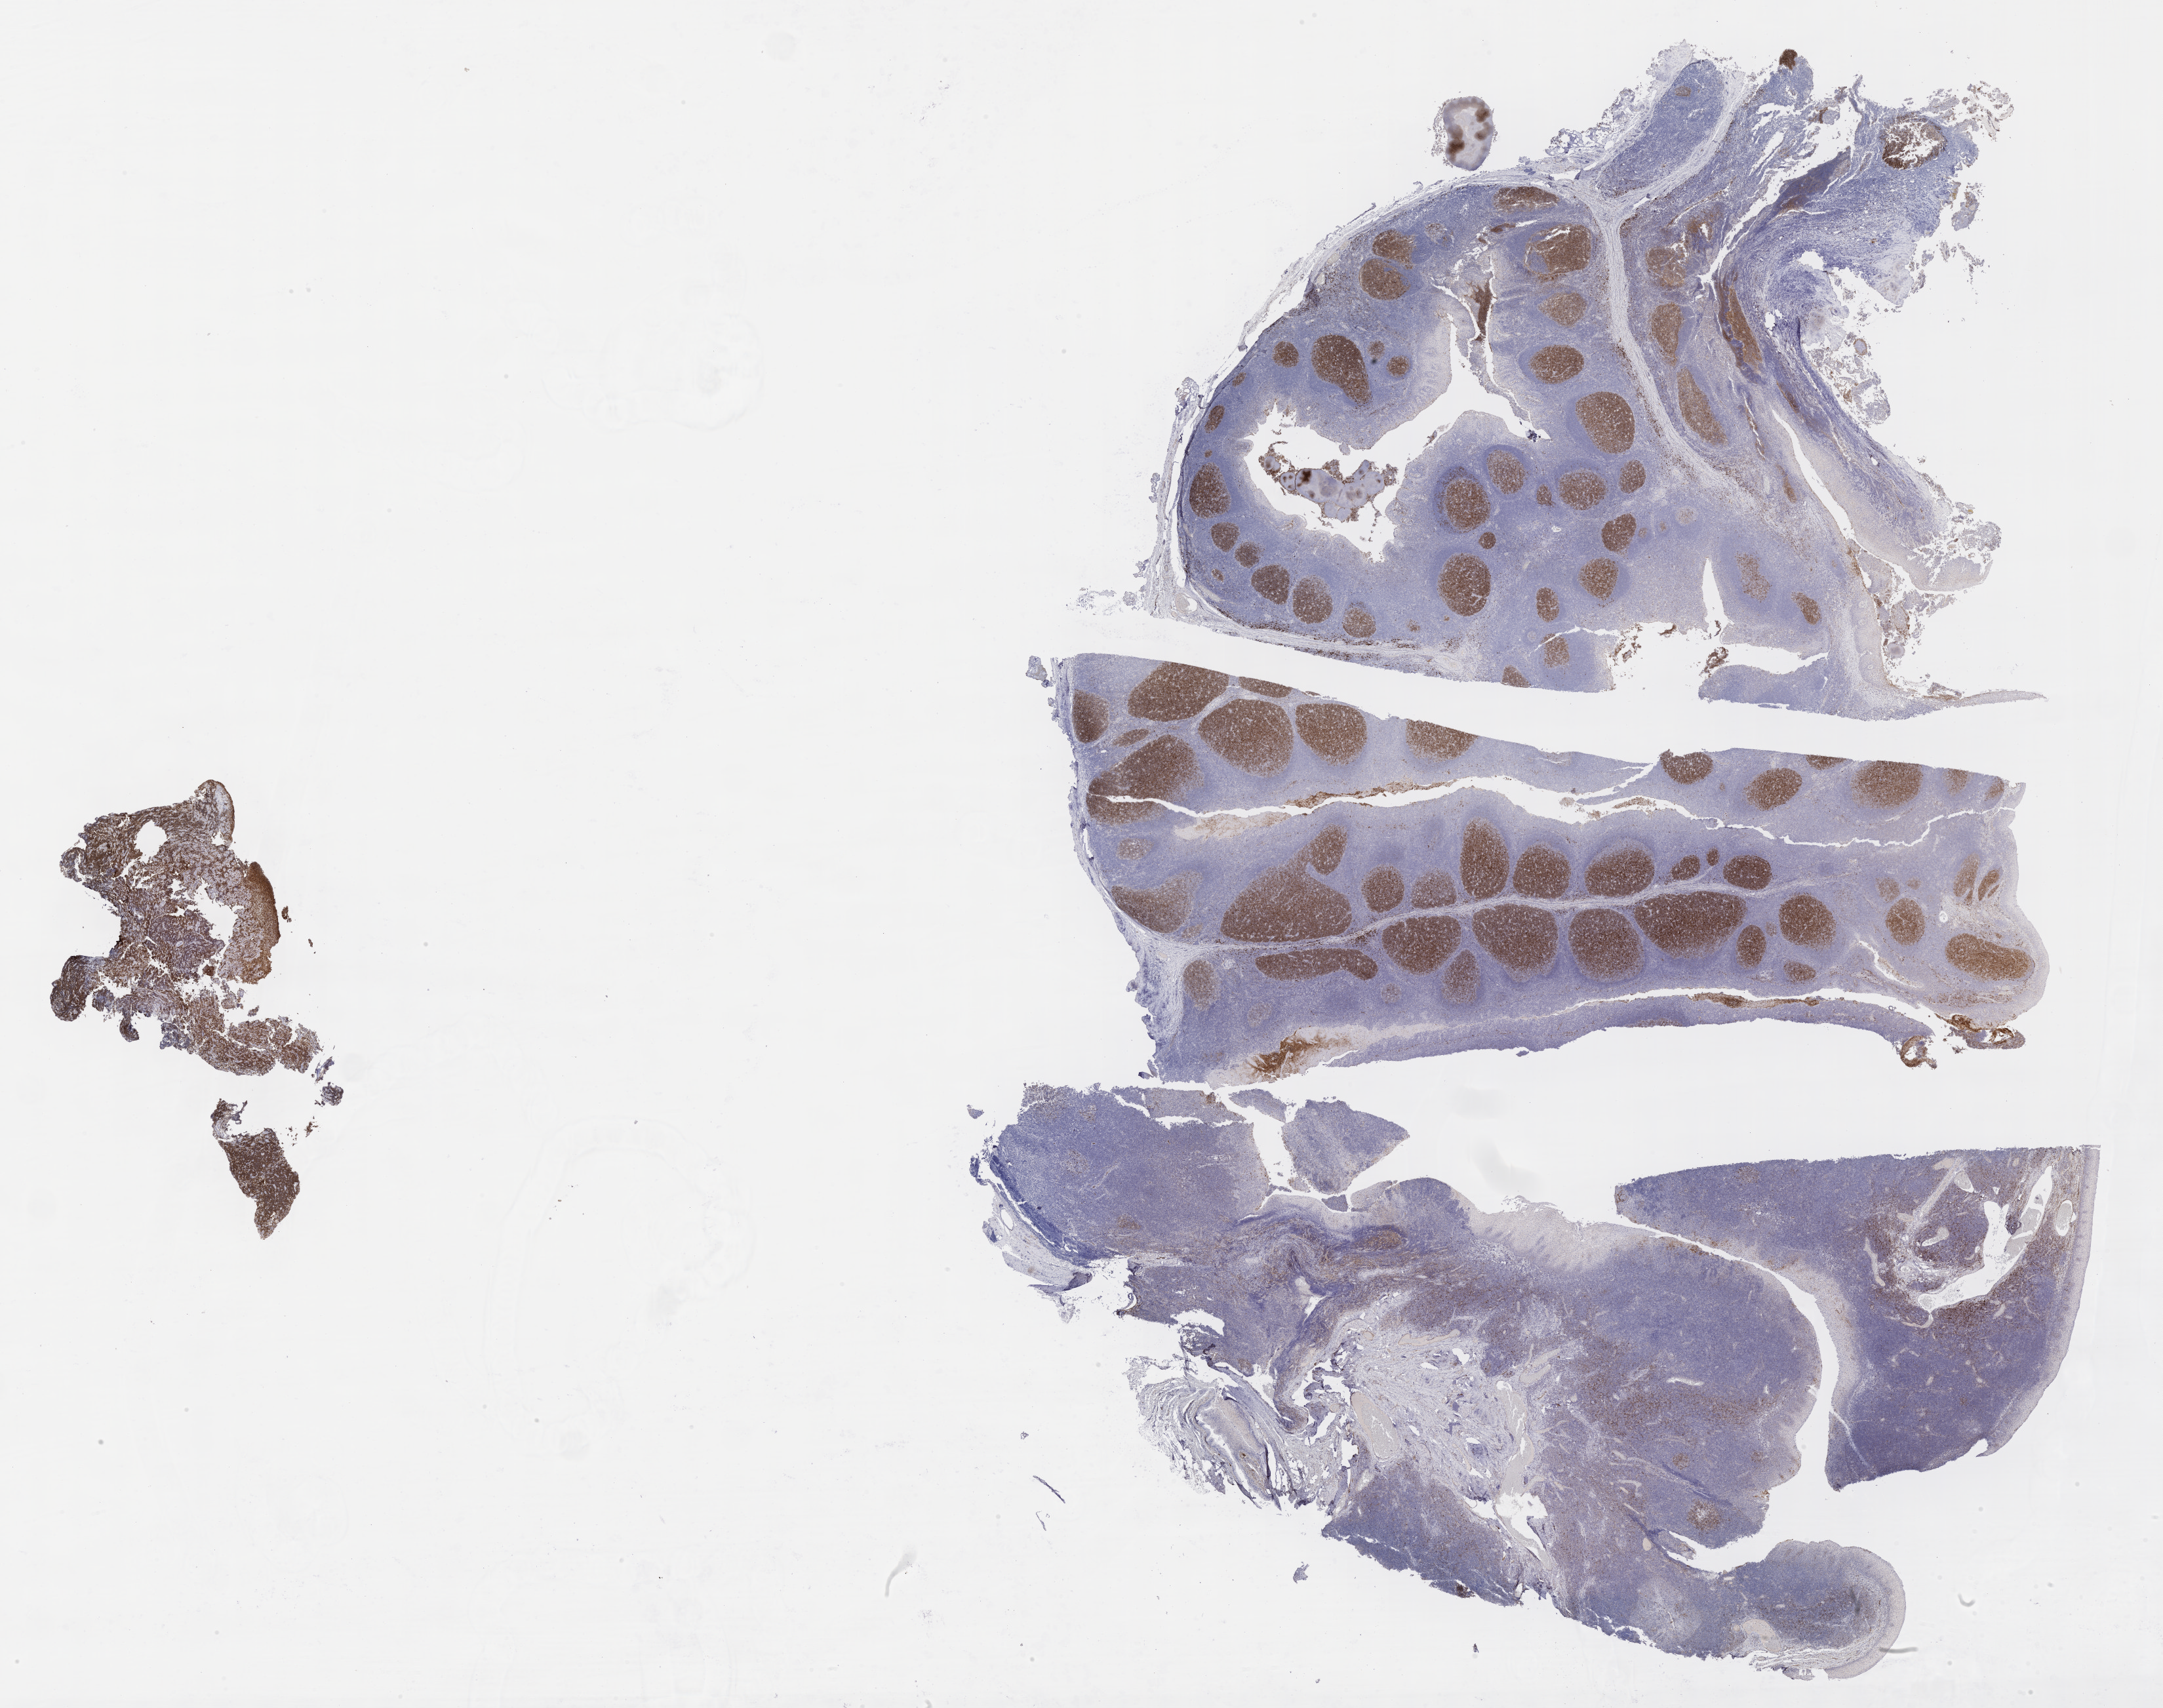
Whole-slide image, immunohistochemical stain for CD10, a low-resolution overview of the entire scanned area, about 26.7 x 21.1 mm; tumor tissue; anatomic site: gum of mandible. Patient male; 10 years old.
Histologic diagnosis: Burkitt lymphoma, NOS.